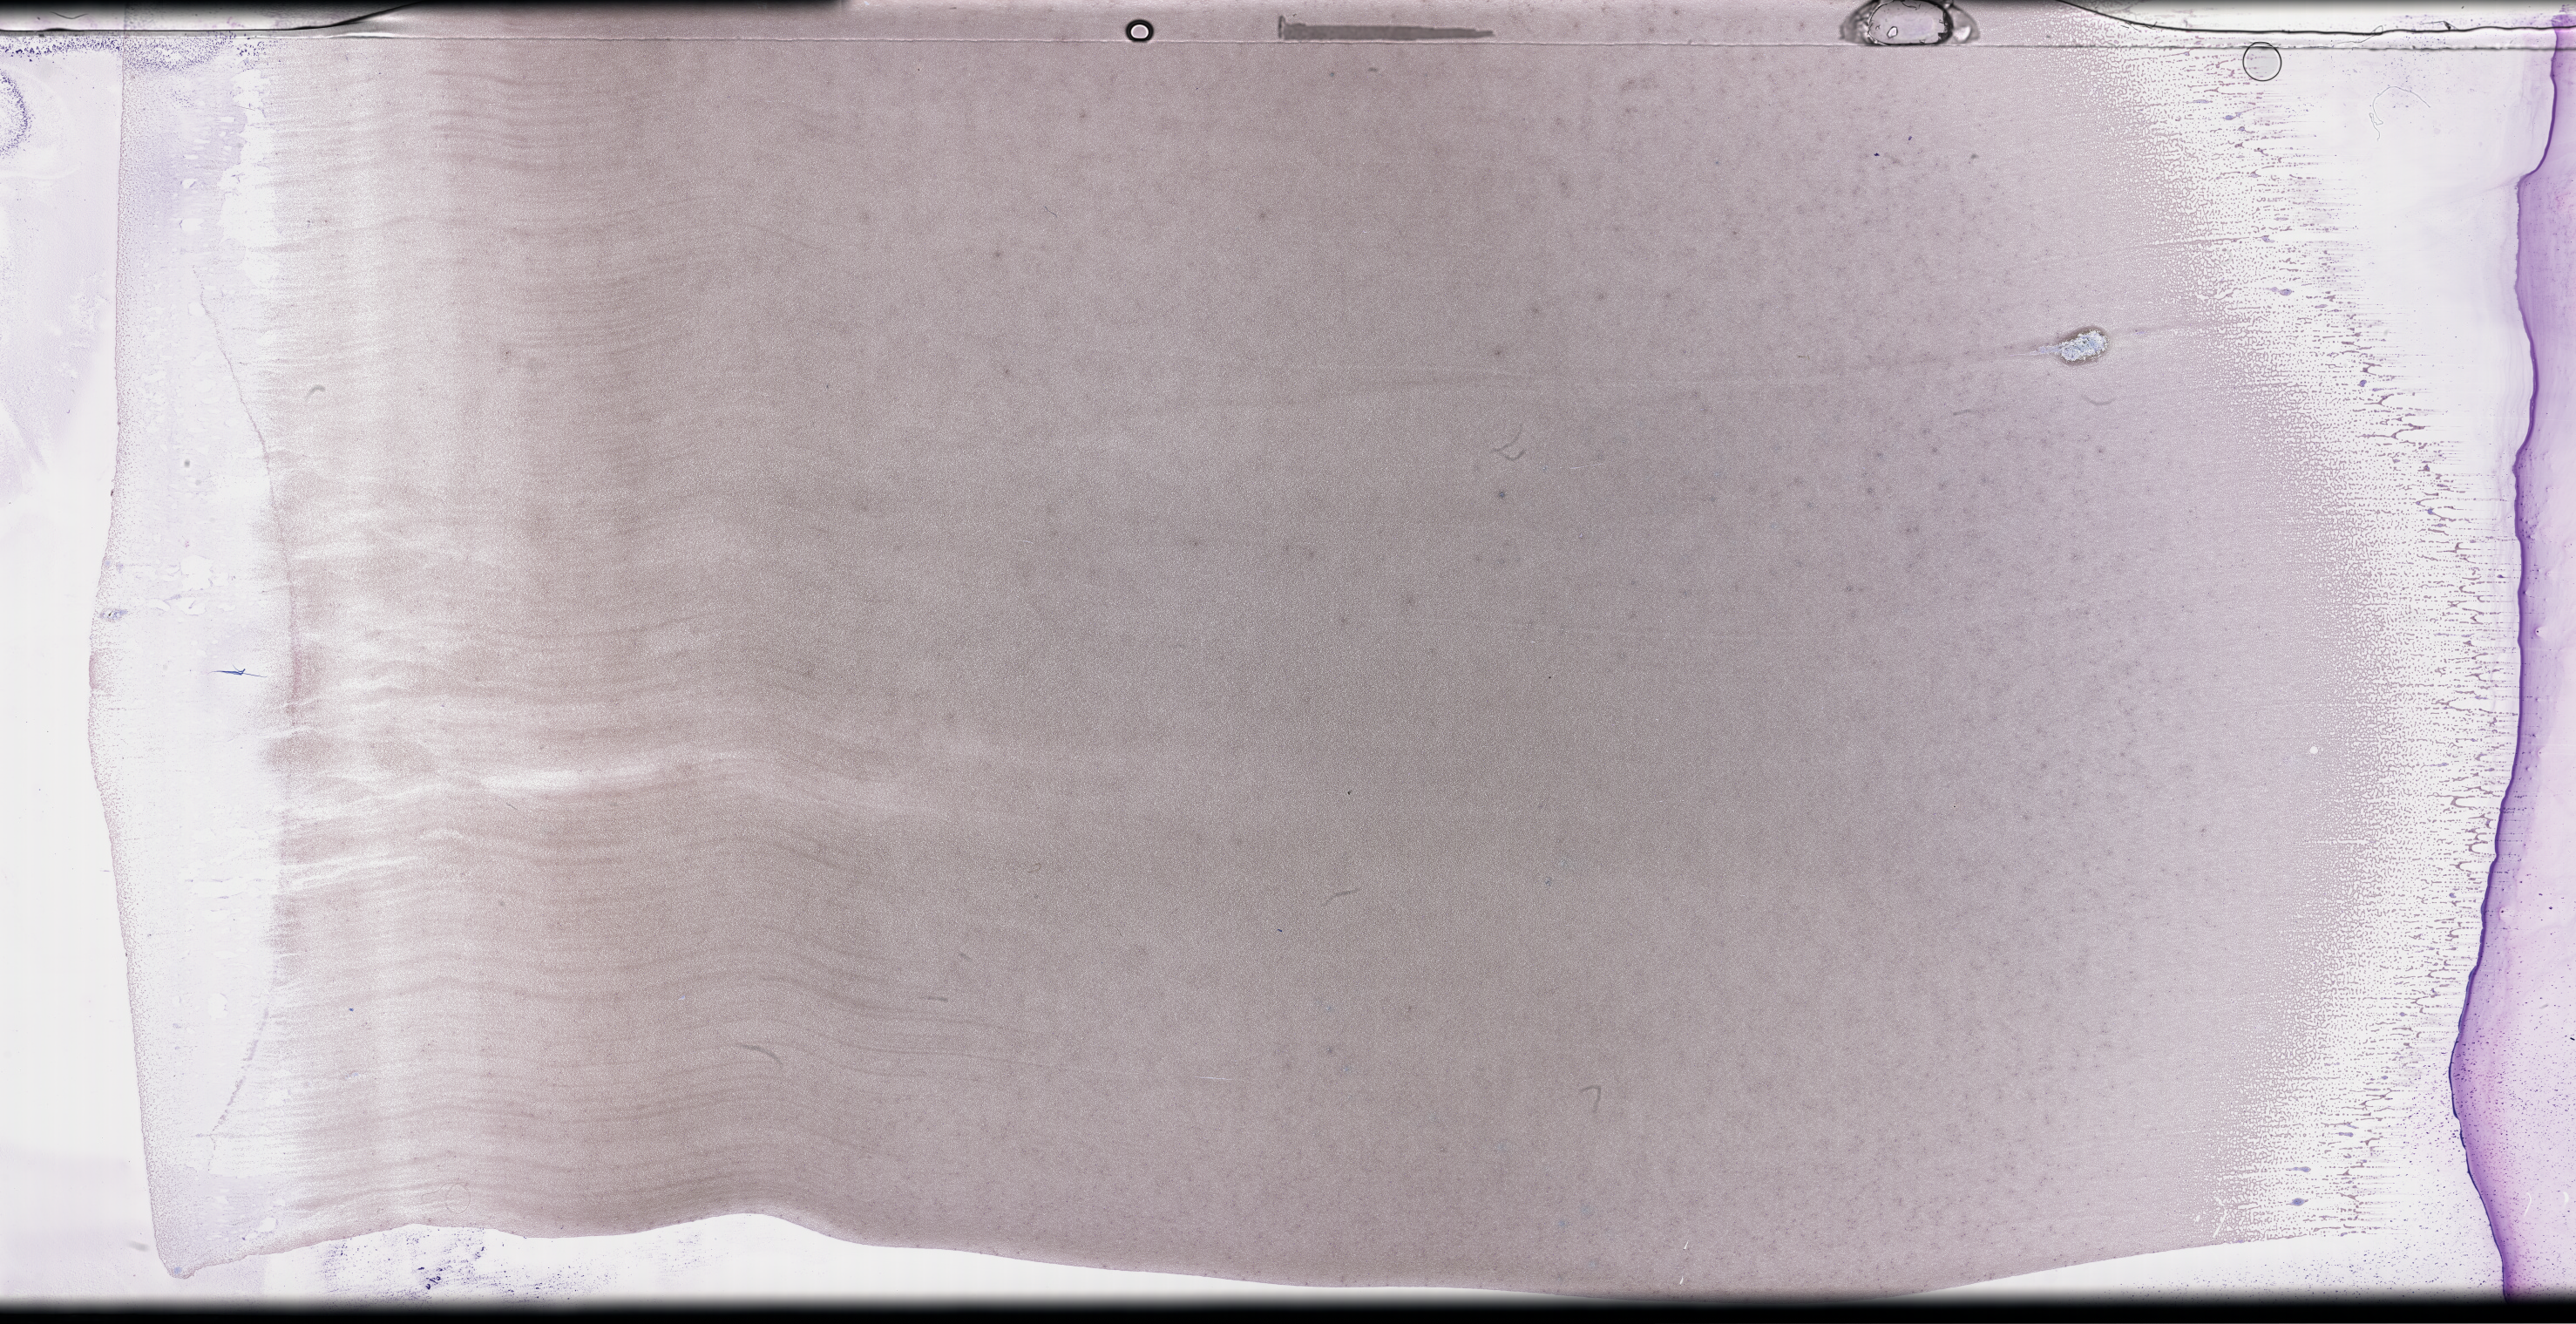
Whole-slide image of a whole blood smear, Wright–Giemsa stain — low-resolution overview of the scanned area, about 47.7 x 24.5 mm, smear from an EDTA sample, specimen time point: collected on treatment. Patient sex: male.
• patient diagnosis: Plasma Cell Myeloma